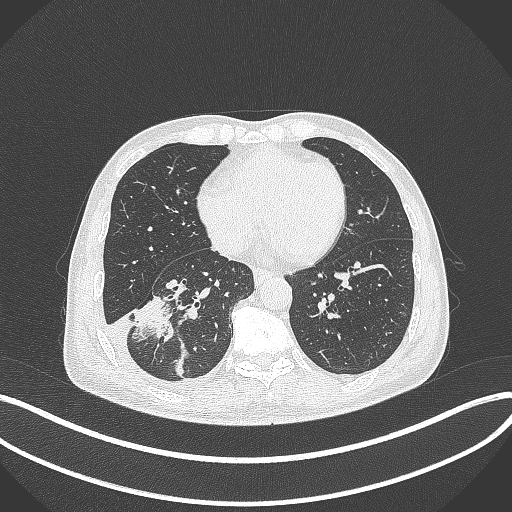
Chest CT, one axial slice. Position 139 of 388 along the scan axis. 120 kVp. Lung window (W 1500 / L -600 HU). 1 mm slice thickness. 512 × 512 image matrix, field of view 400 × 400 mm. Patient: male, 64 years. From the clinical record (not read from this slice): clinical TNM (as recorded): T3 N0 M0; histopathological grade: G2-3.
Annotated regions visible in this slice (rectangle marked by the reading radiologist):
- lung tumour (recorded histology: adenocarcinoma): bounding box <127,294,179,348> (left, top, right, bottom; pixels)